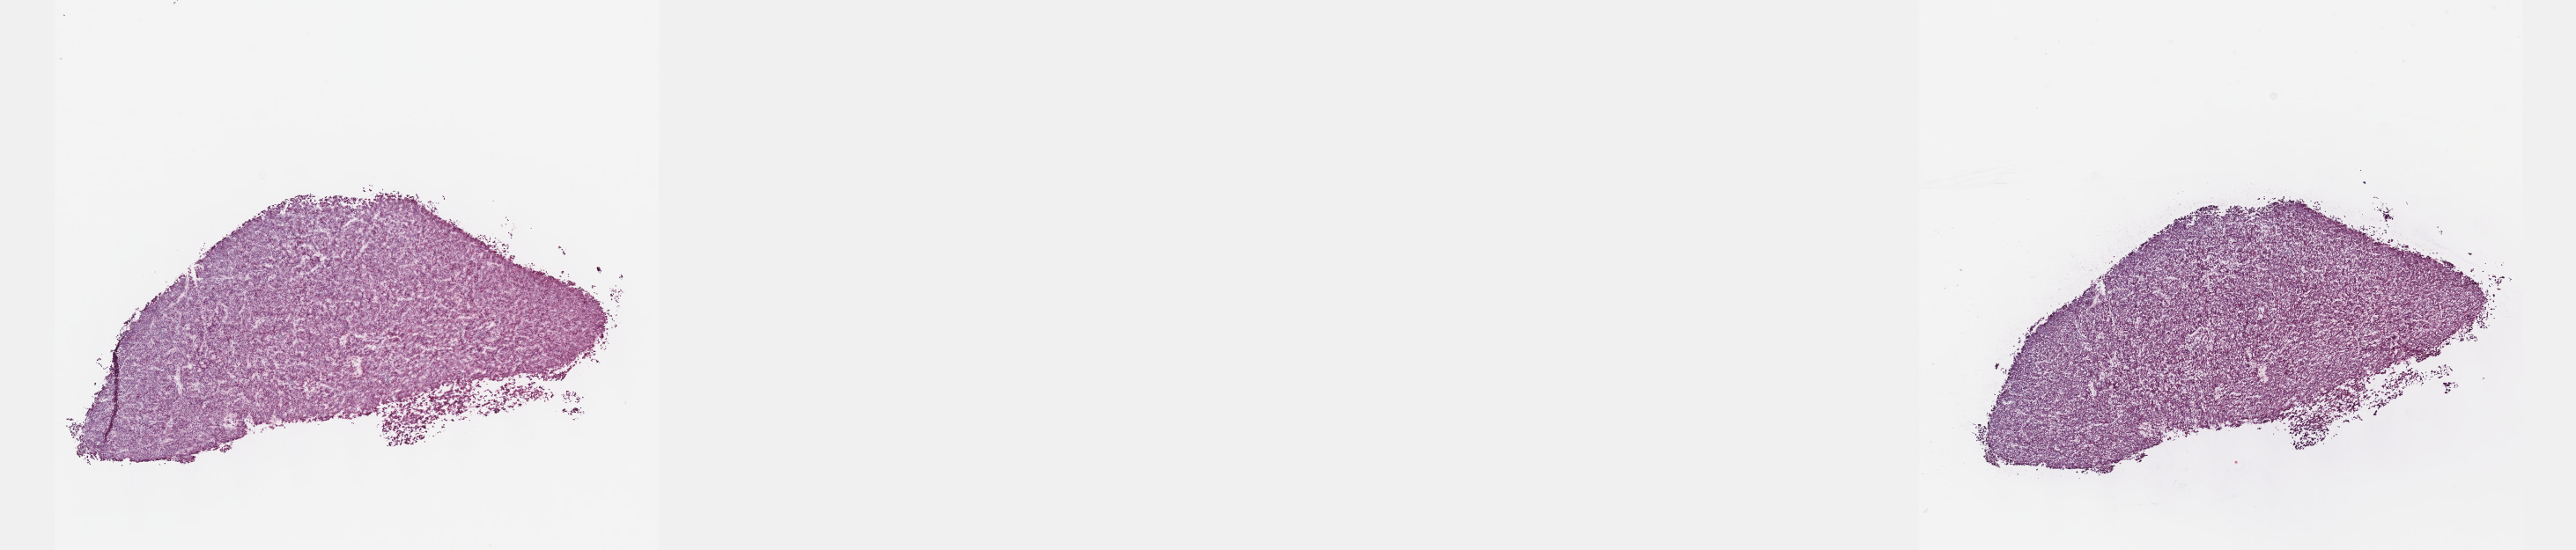
Hematoxylin and eosin (H&E) stained whole-slide image, low-resolution overview of the scanned area, about 23.6 x 5.1 mm (from a 40x scan); frozen section; primary tumour sample from the liver. Female patient; age at initial diagnosis 47 years. Histologic grade: G3 (poorly differentiated). Pathologist review of this section (percent, as recorded): tumour cells 90%, tumour nuclei 95%, normal cells 0%, stromal cells 10%, necrosis 0%. Infiltration values recorded for this section: lymphocyte infiltration 0%, monocyte infiltration 0%, neutrophil infiltration 0%.
AJCC pathologic stage: I. Diagnosis: Hepatocellular carcinoma, NOS.